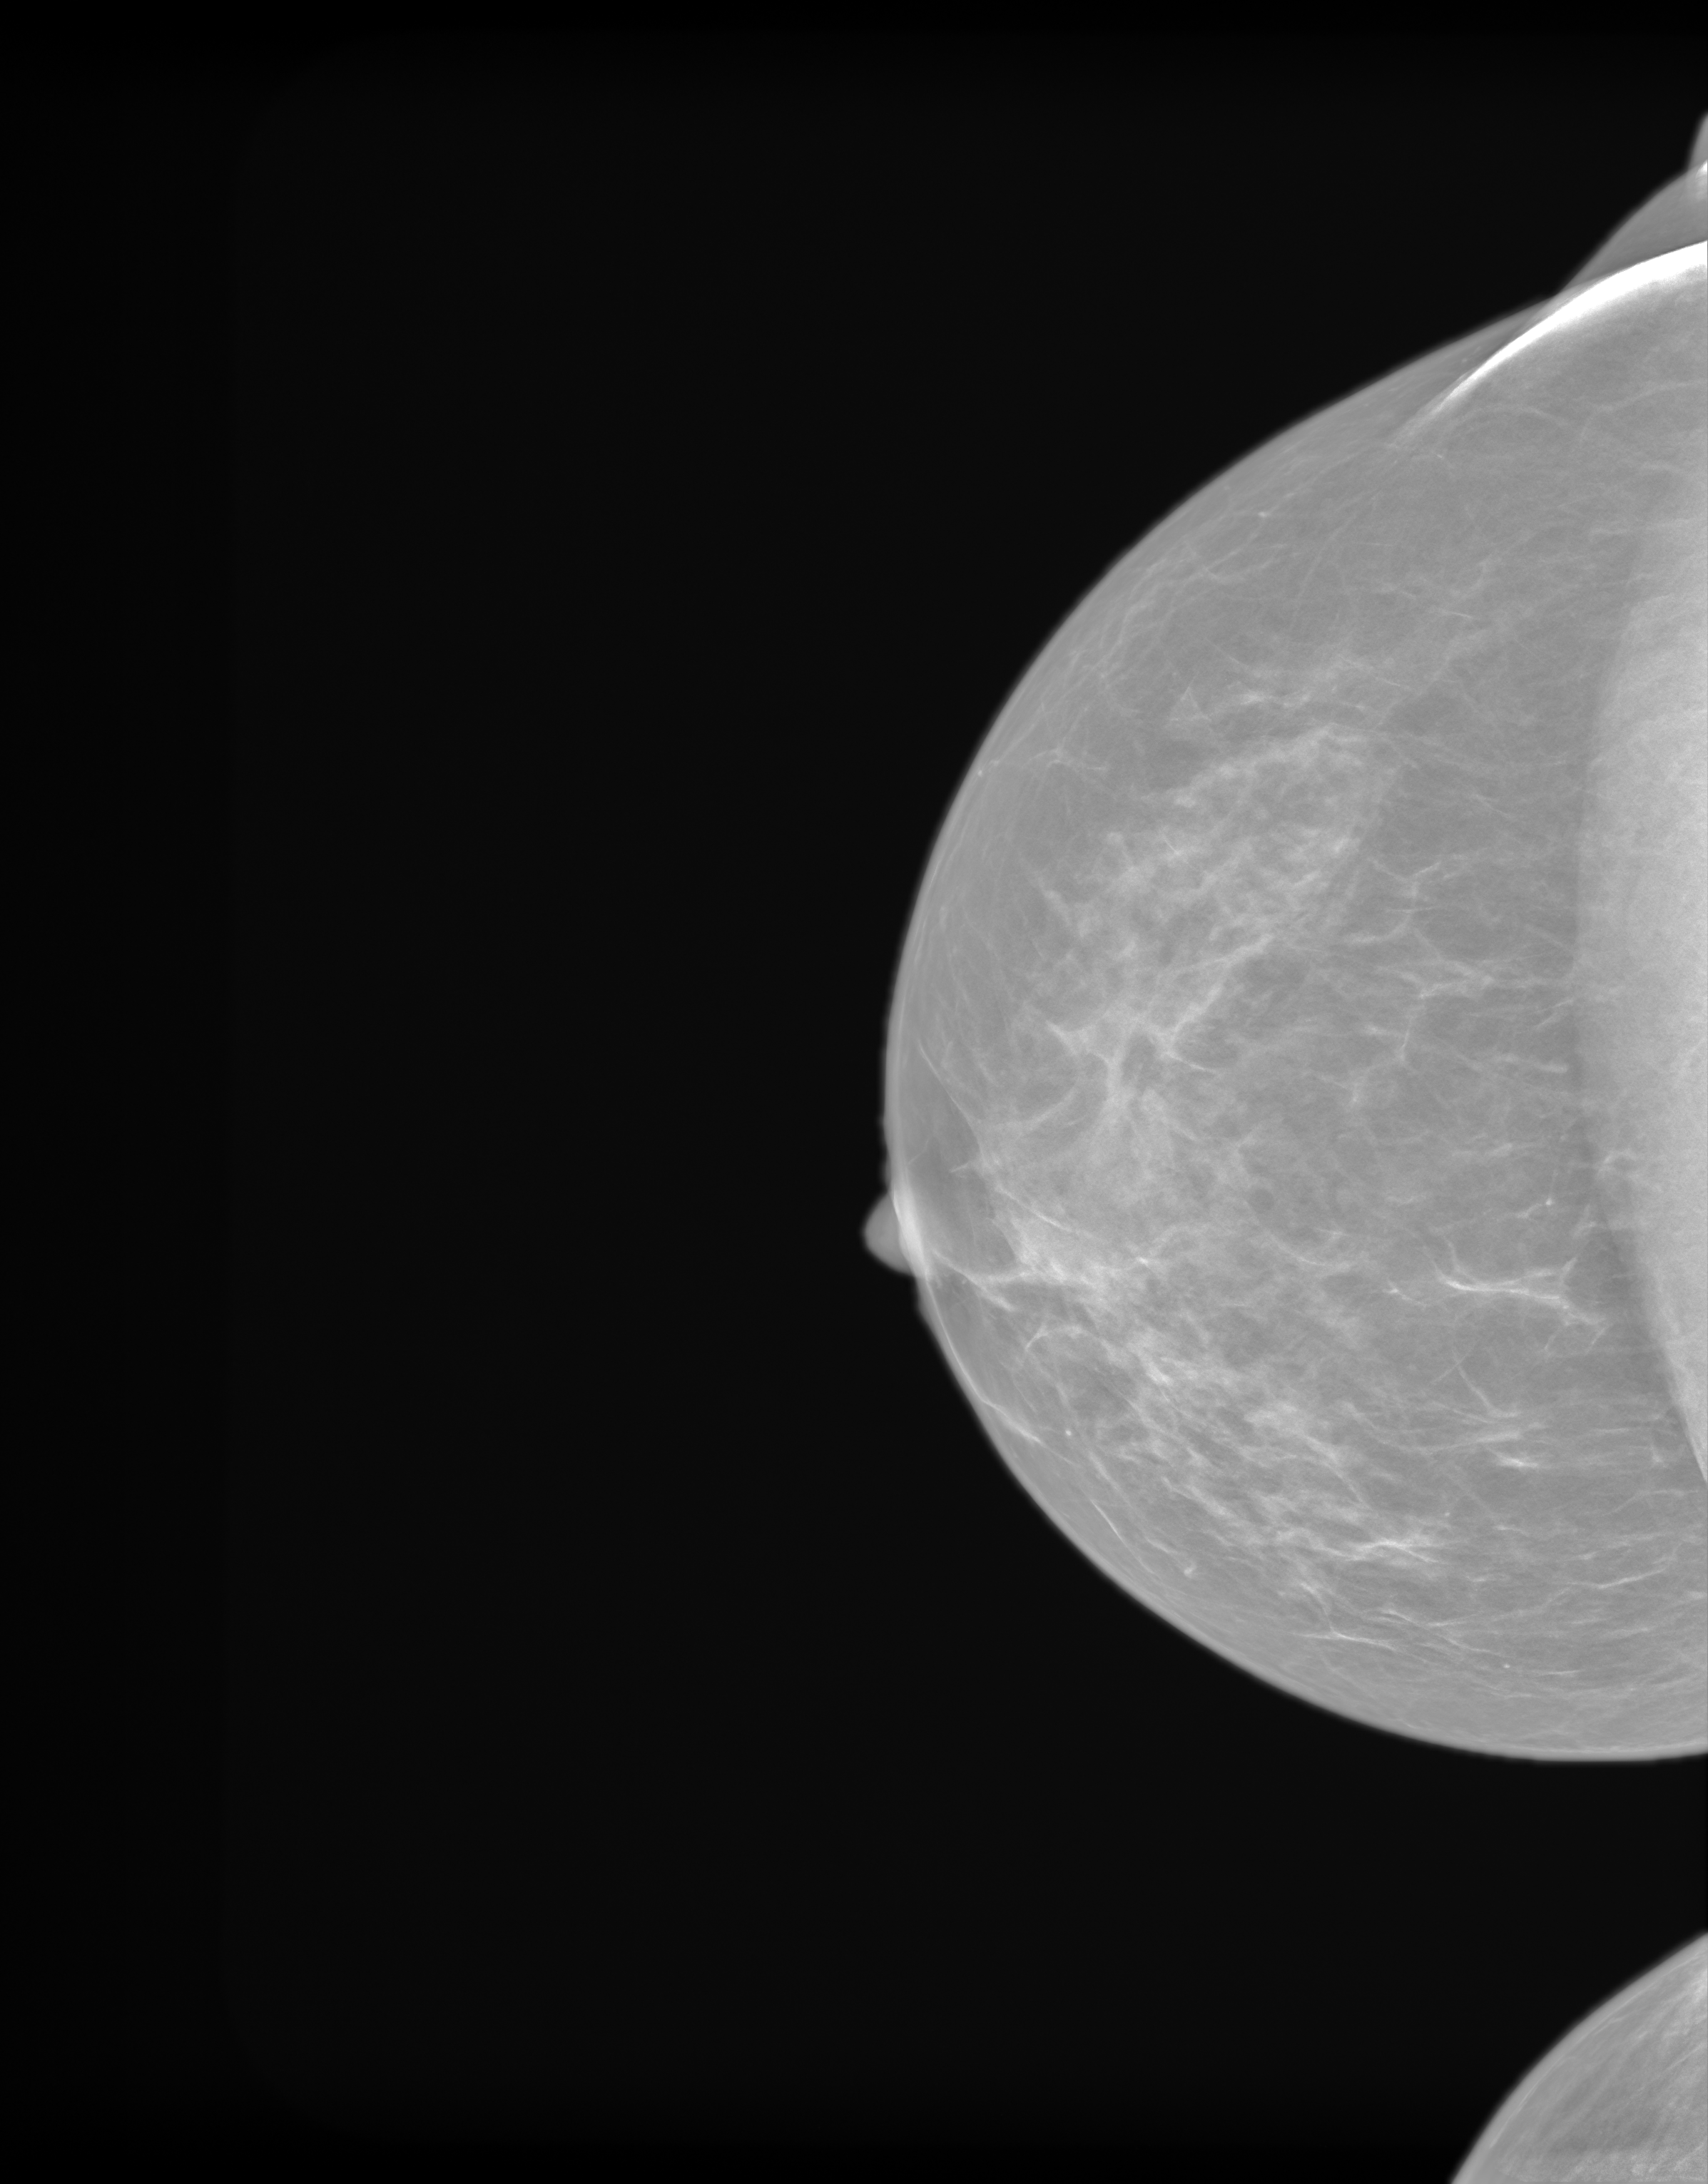
Annual screening mammography examination. Female patient, age 54 years.
Image type: synthesized 2-D view from tomosynthesis. Breast: right. Projection: cranio-caudal projection.